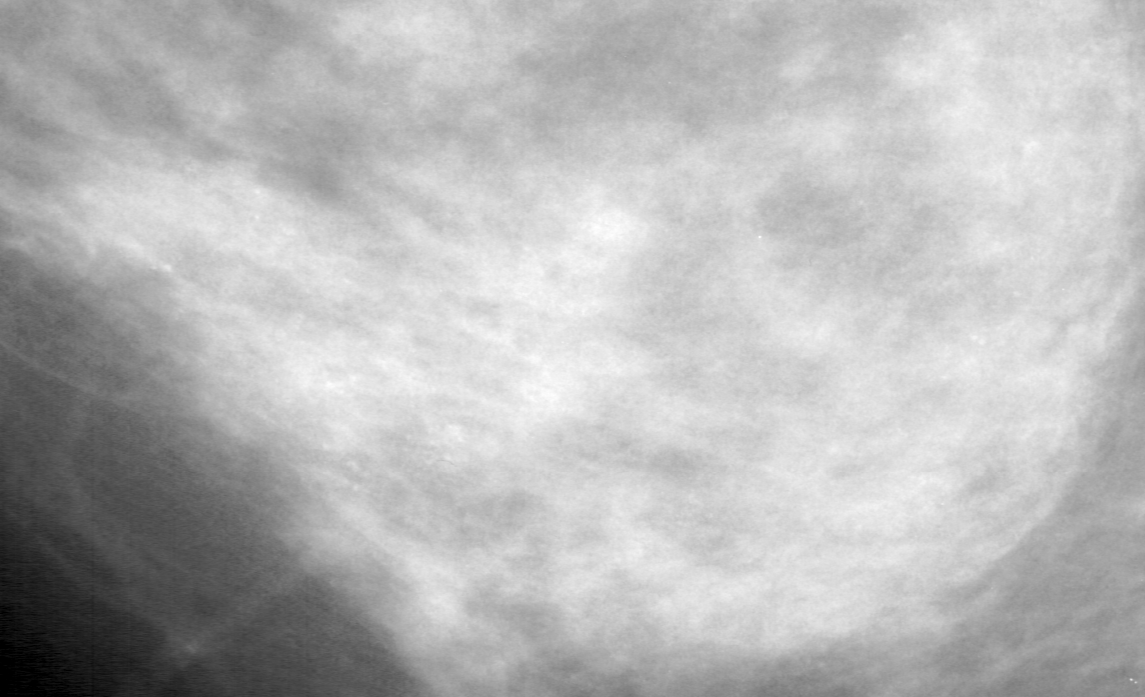
Cropped region of a digitized screen-film mammogram centred on a radiologist-marked abnormality, left breast, CC view.
- Marked abnormality: calcifications, morphology pleomorphic, distribution segmental; BI-RADS assessment category 4; subtlety rating 2 on a 1 (subtle) to 5 (obvious) scale; pathology (as recorded): benign.